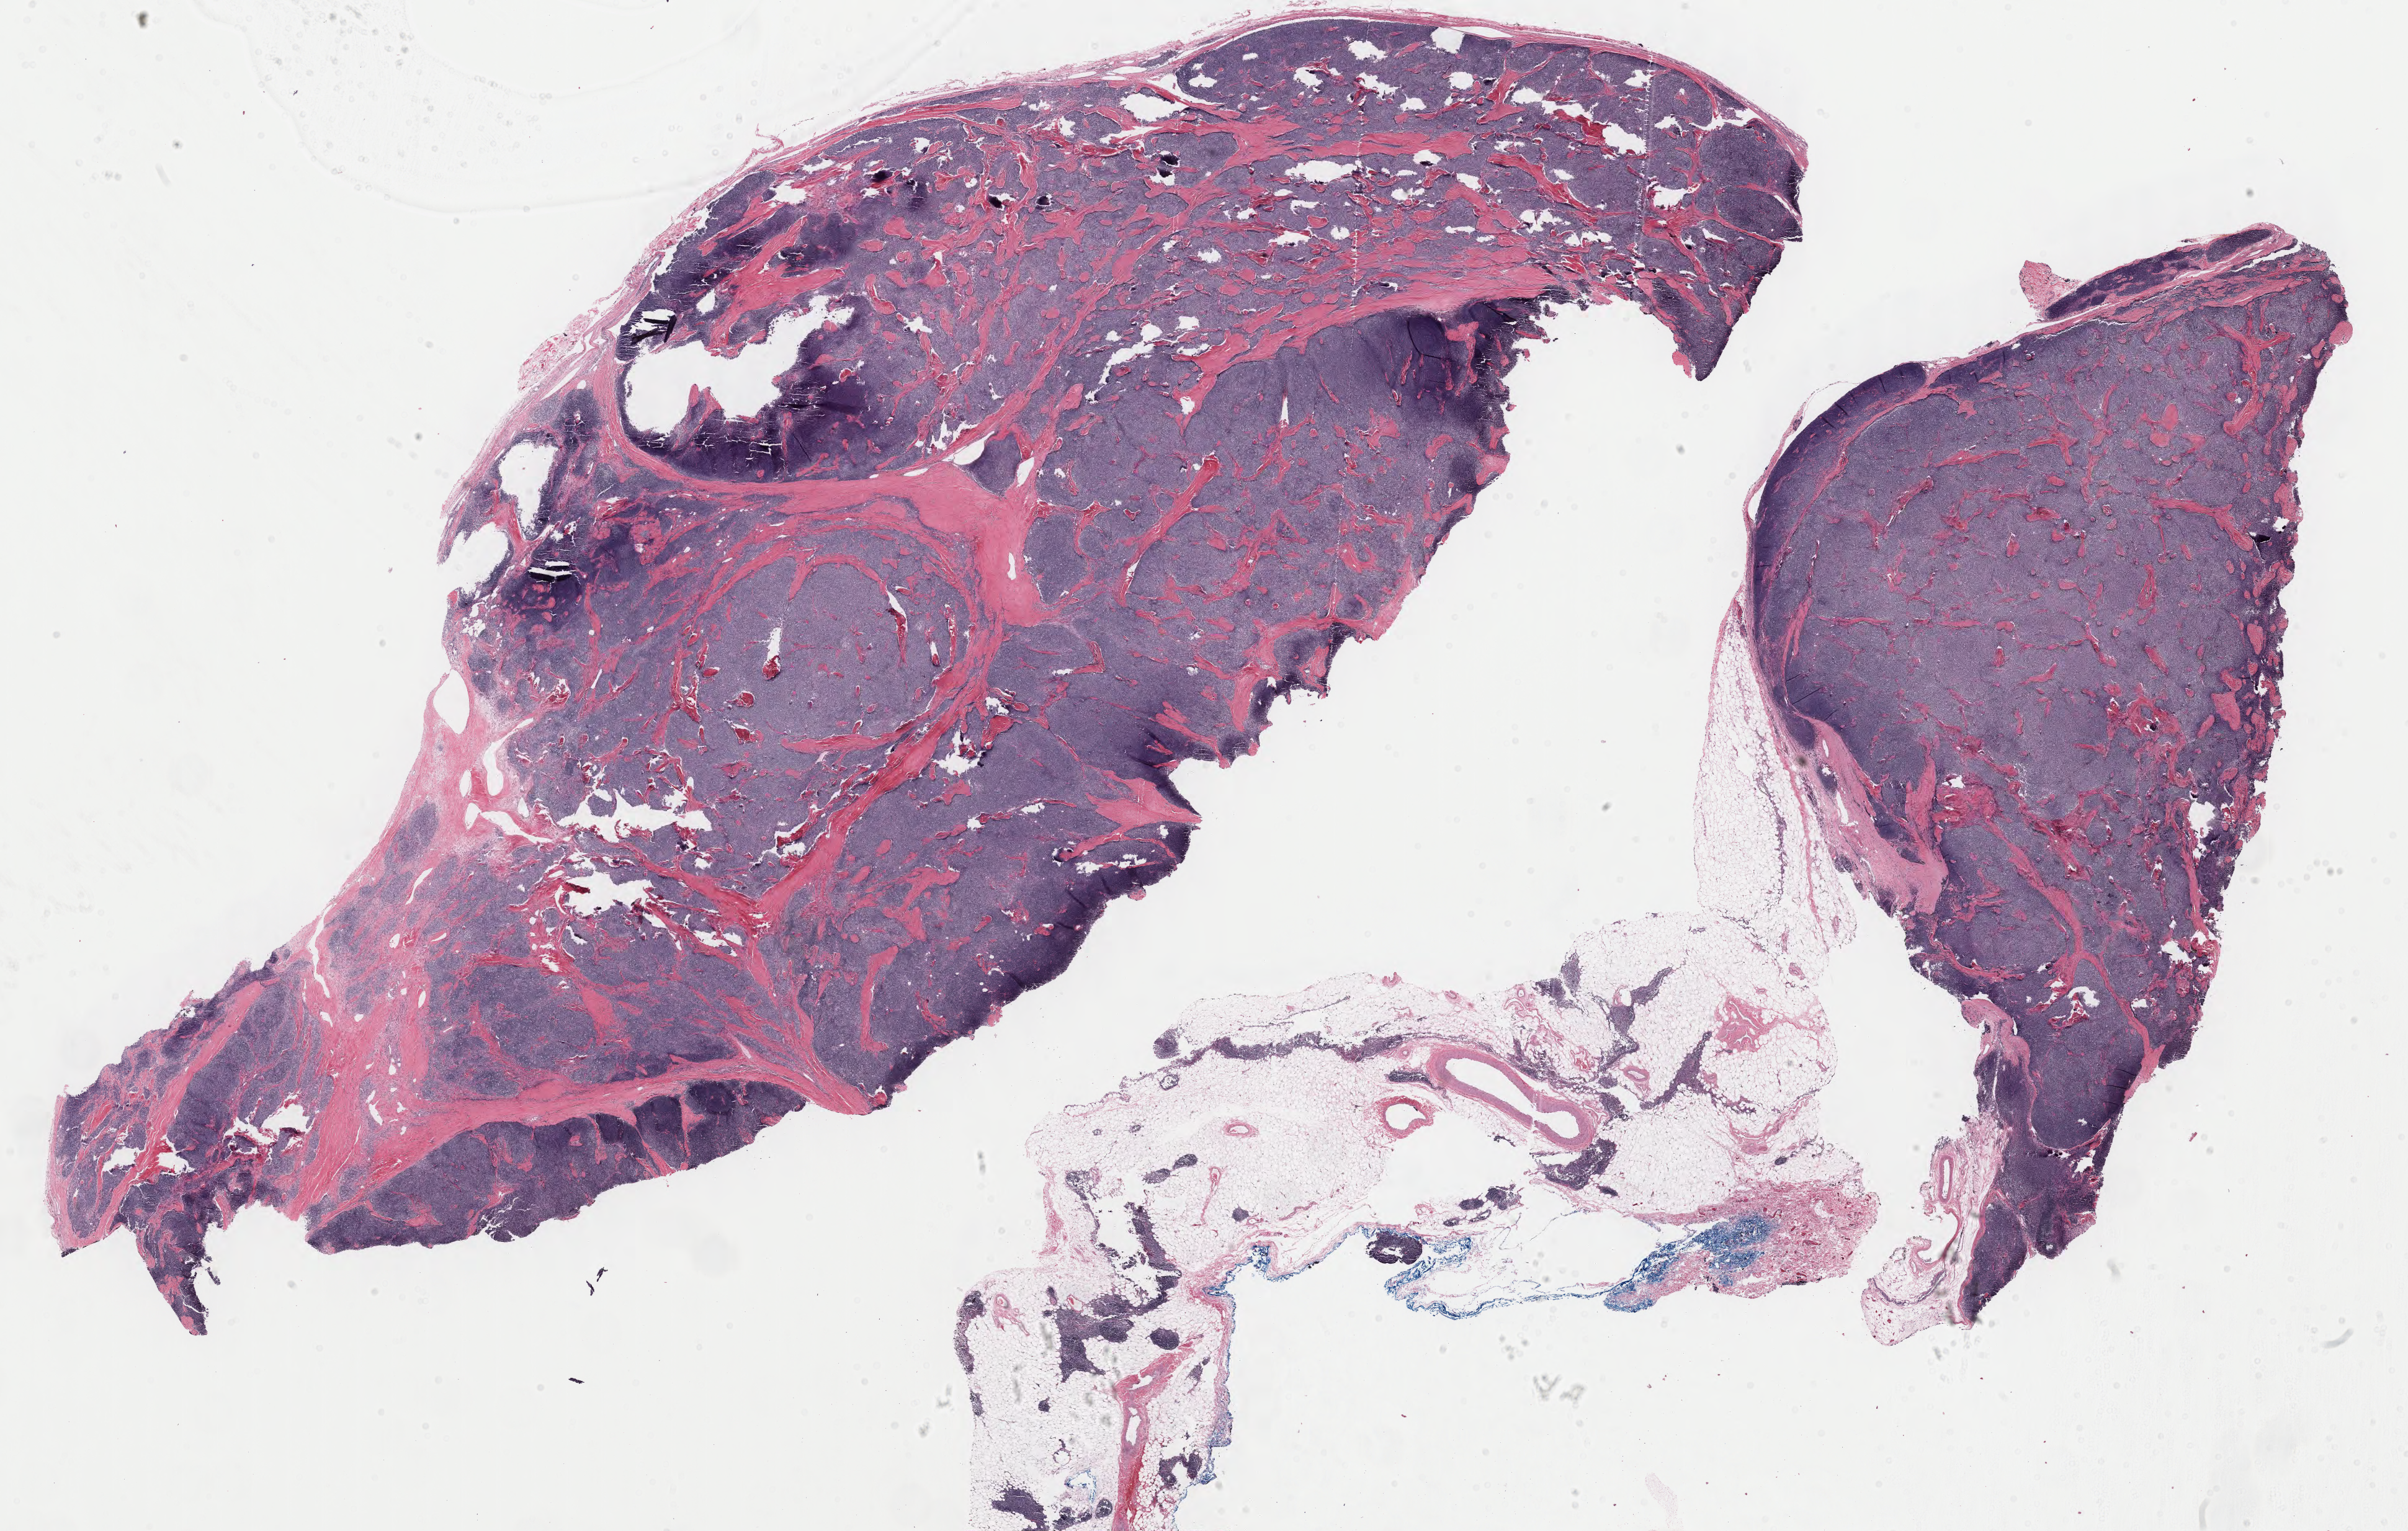
Digitized Hematoxylin and eosin (H&E) stained tissue section (whole slide), shown as a low-resolution overview of the whole scanned area (about 30.8 x 19.6 mm, from a 40x scan), FFPE section, primary tumour sample from the thymus. Female, age 50 years at initial diagnosis.
Histologic diagnosis: Thymoma, type AB, malignant.